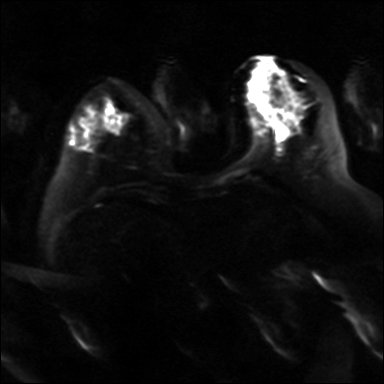
Breast MRI, one axial slice; slice 9 of 36 in the series (ordered by position); diffusion-weighted series; image 2 of 4 stored at this slice position (different b-values; order by instance number); 3 T; 4 mm slice thickness; 384 × 384 image matrix, field of view 320 × 320 mm. Female patient.
Structures marked on this image (expert manual segmentation):
- tumour on diffusion-weighted imaging: bounding box [x1, y1, x2, y2] px = [270, 118, 279, 124]